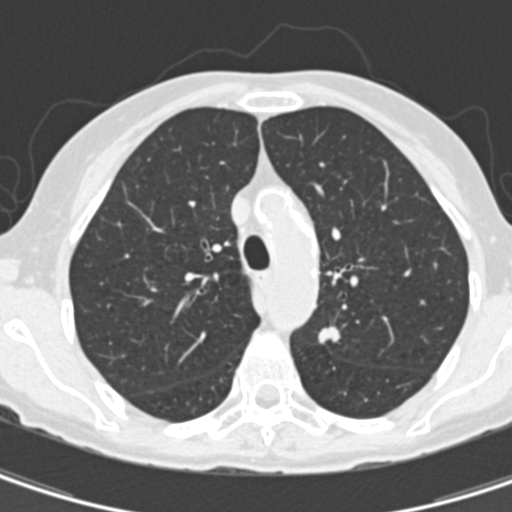
Low-dose screening chest CT, one axial slice; slice 110 of 157 in the series (ordered by position); 120 kVp; lung window (W 1500 / L -600 HU); 2 mm slice thickness; 512 × 512 image matrix, field of view 260 × 260 mm.
Annotated regions visible in this slice (outlined manually by an expert reader):
- lesion 1 (tumor, upper lobe of left lung): bounding box [x1, y1, x2, y2] px = [318, 326, 340, 344]